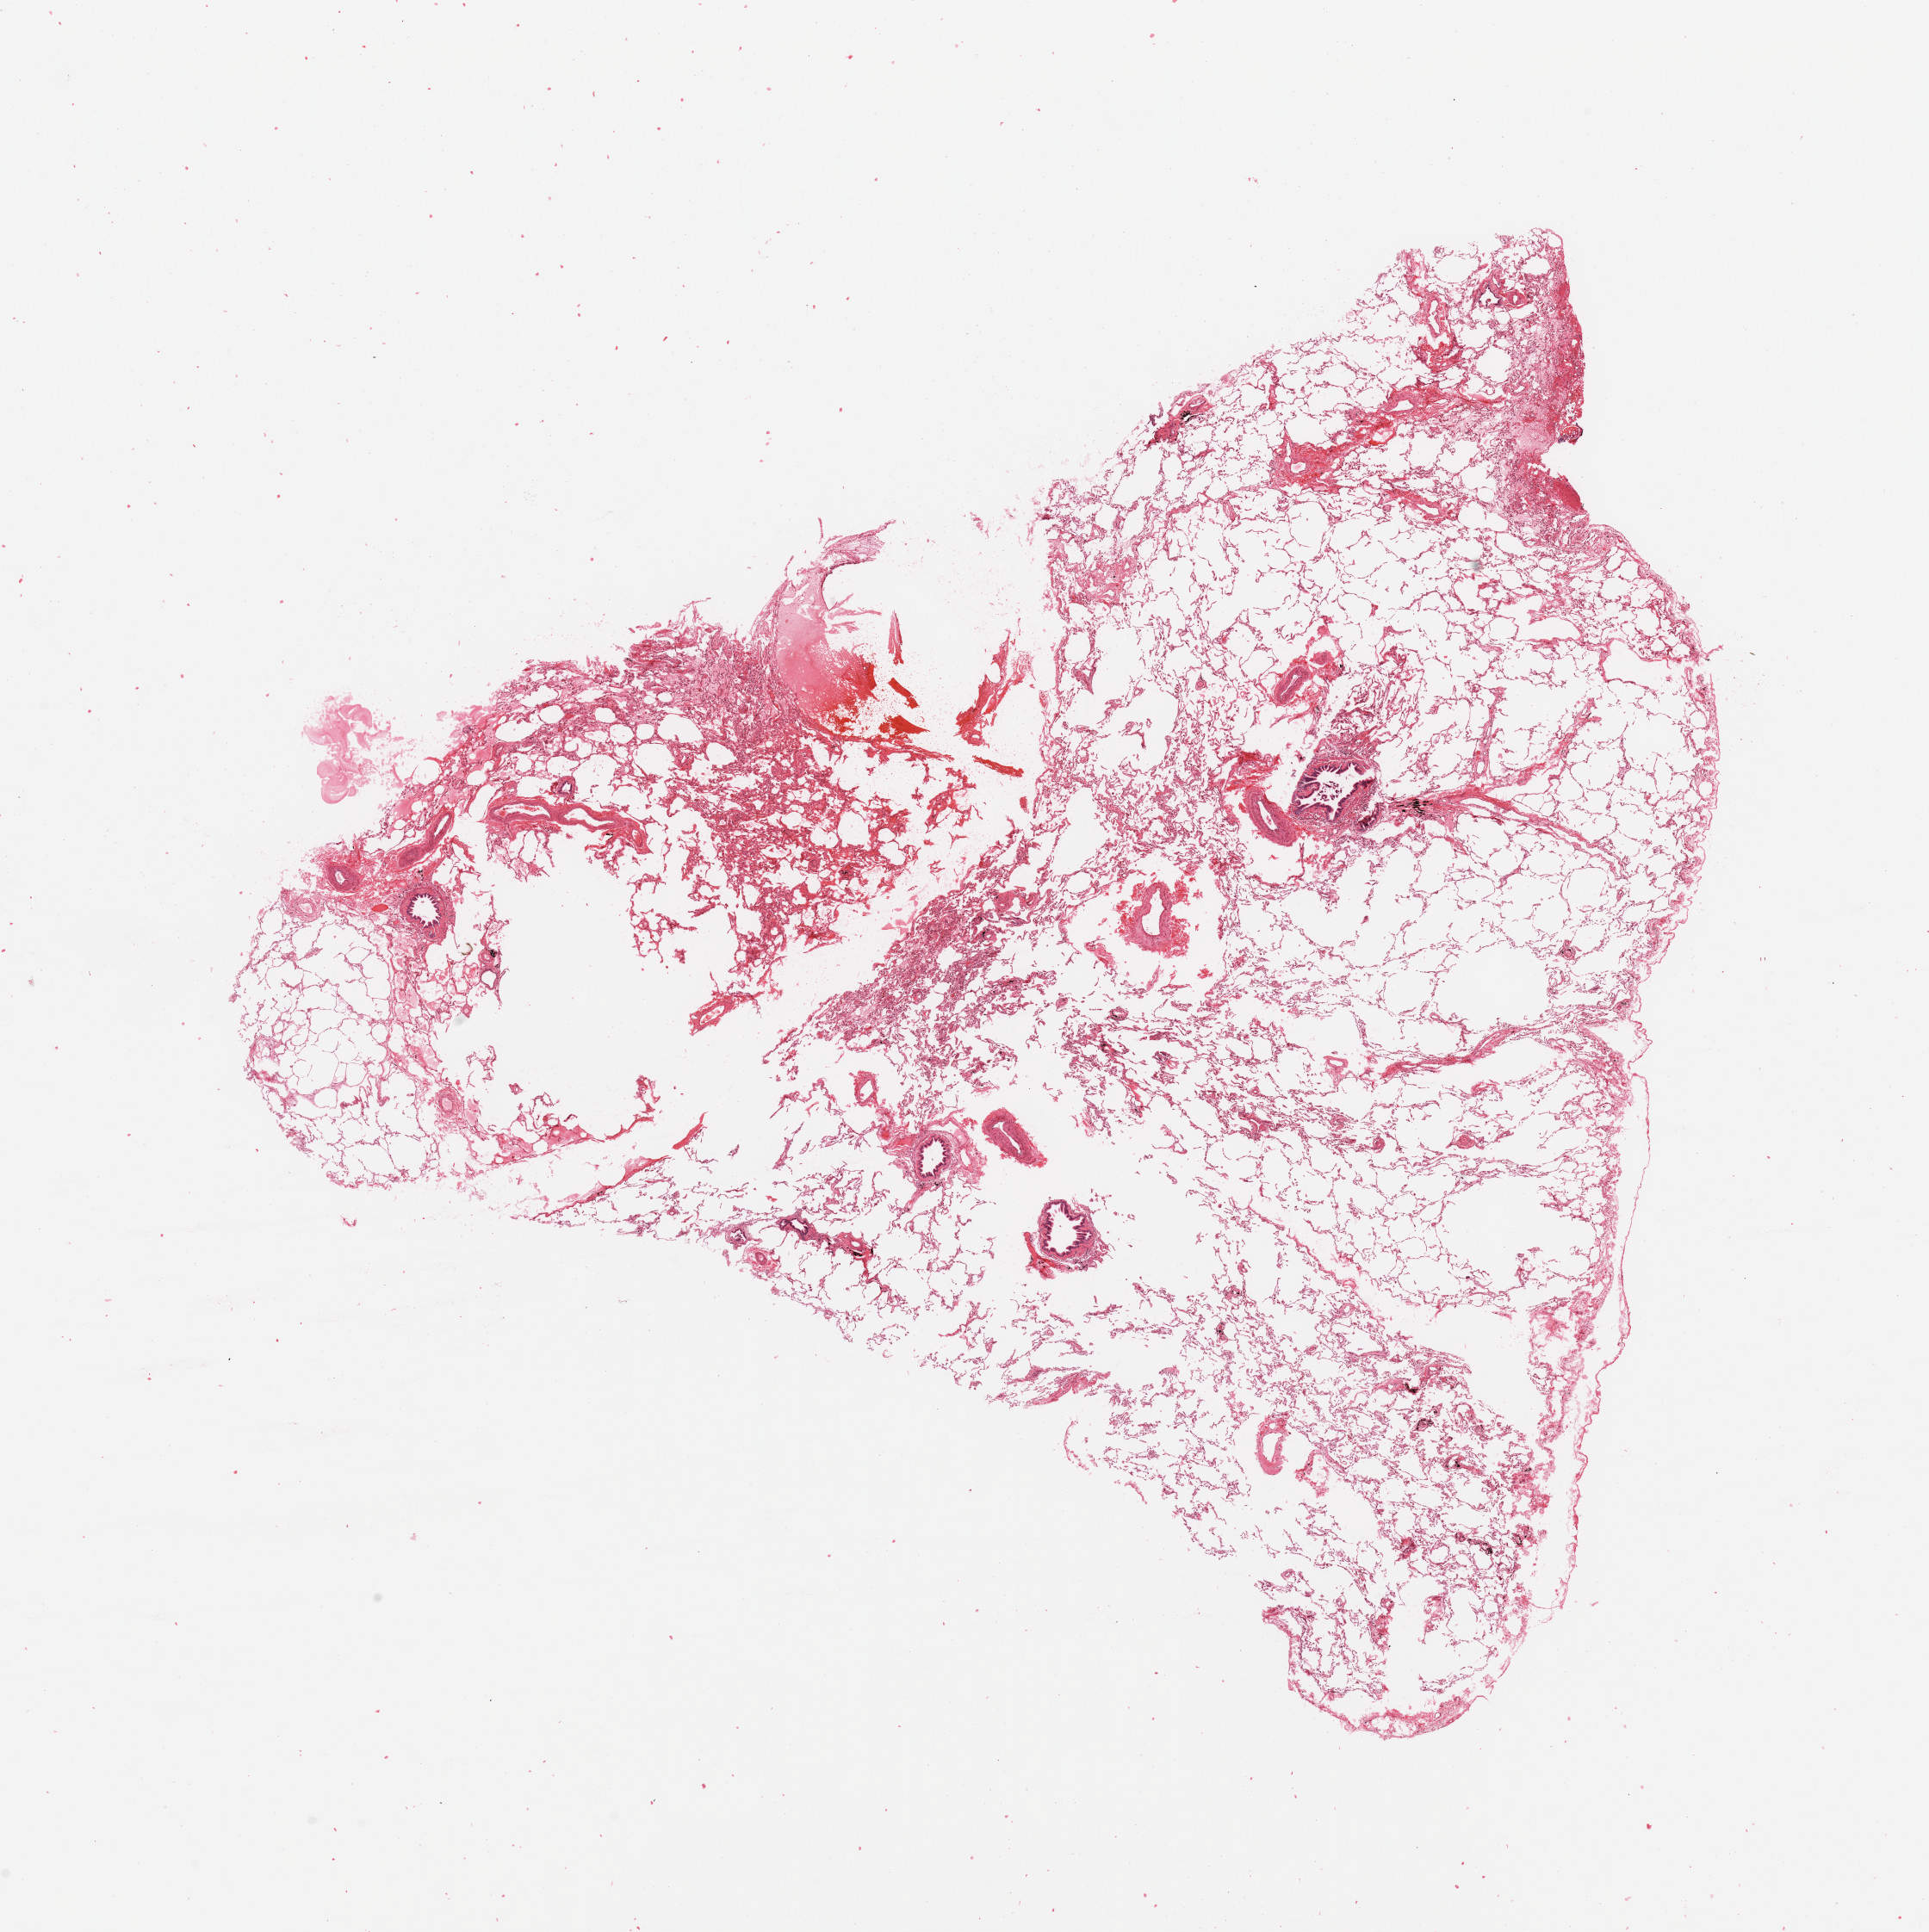
Digitized H&E tissue section (whole slide), whole scanned area (about 17.7 x 17.8 mm, slide scanned at 20x) shown as a low-resolution overview. Normal (non-tumour) tissue sample, sampled site: lung. 59-year-old male patient.
• this section: normal (non-tumour) tissue from the same patient
• patient diagnosis: Adenocarcinoma, NOS